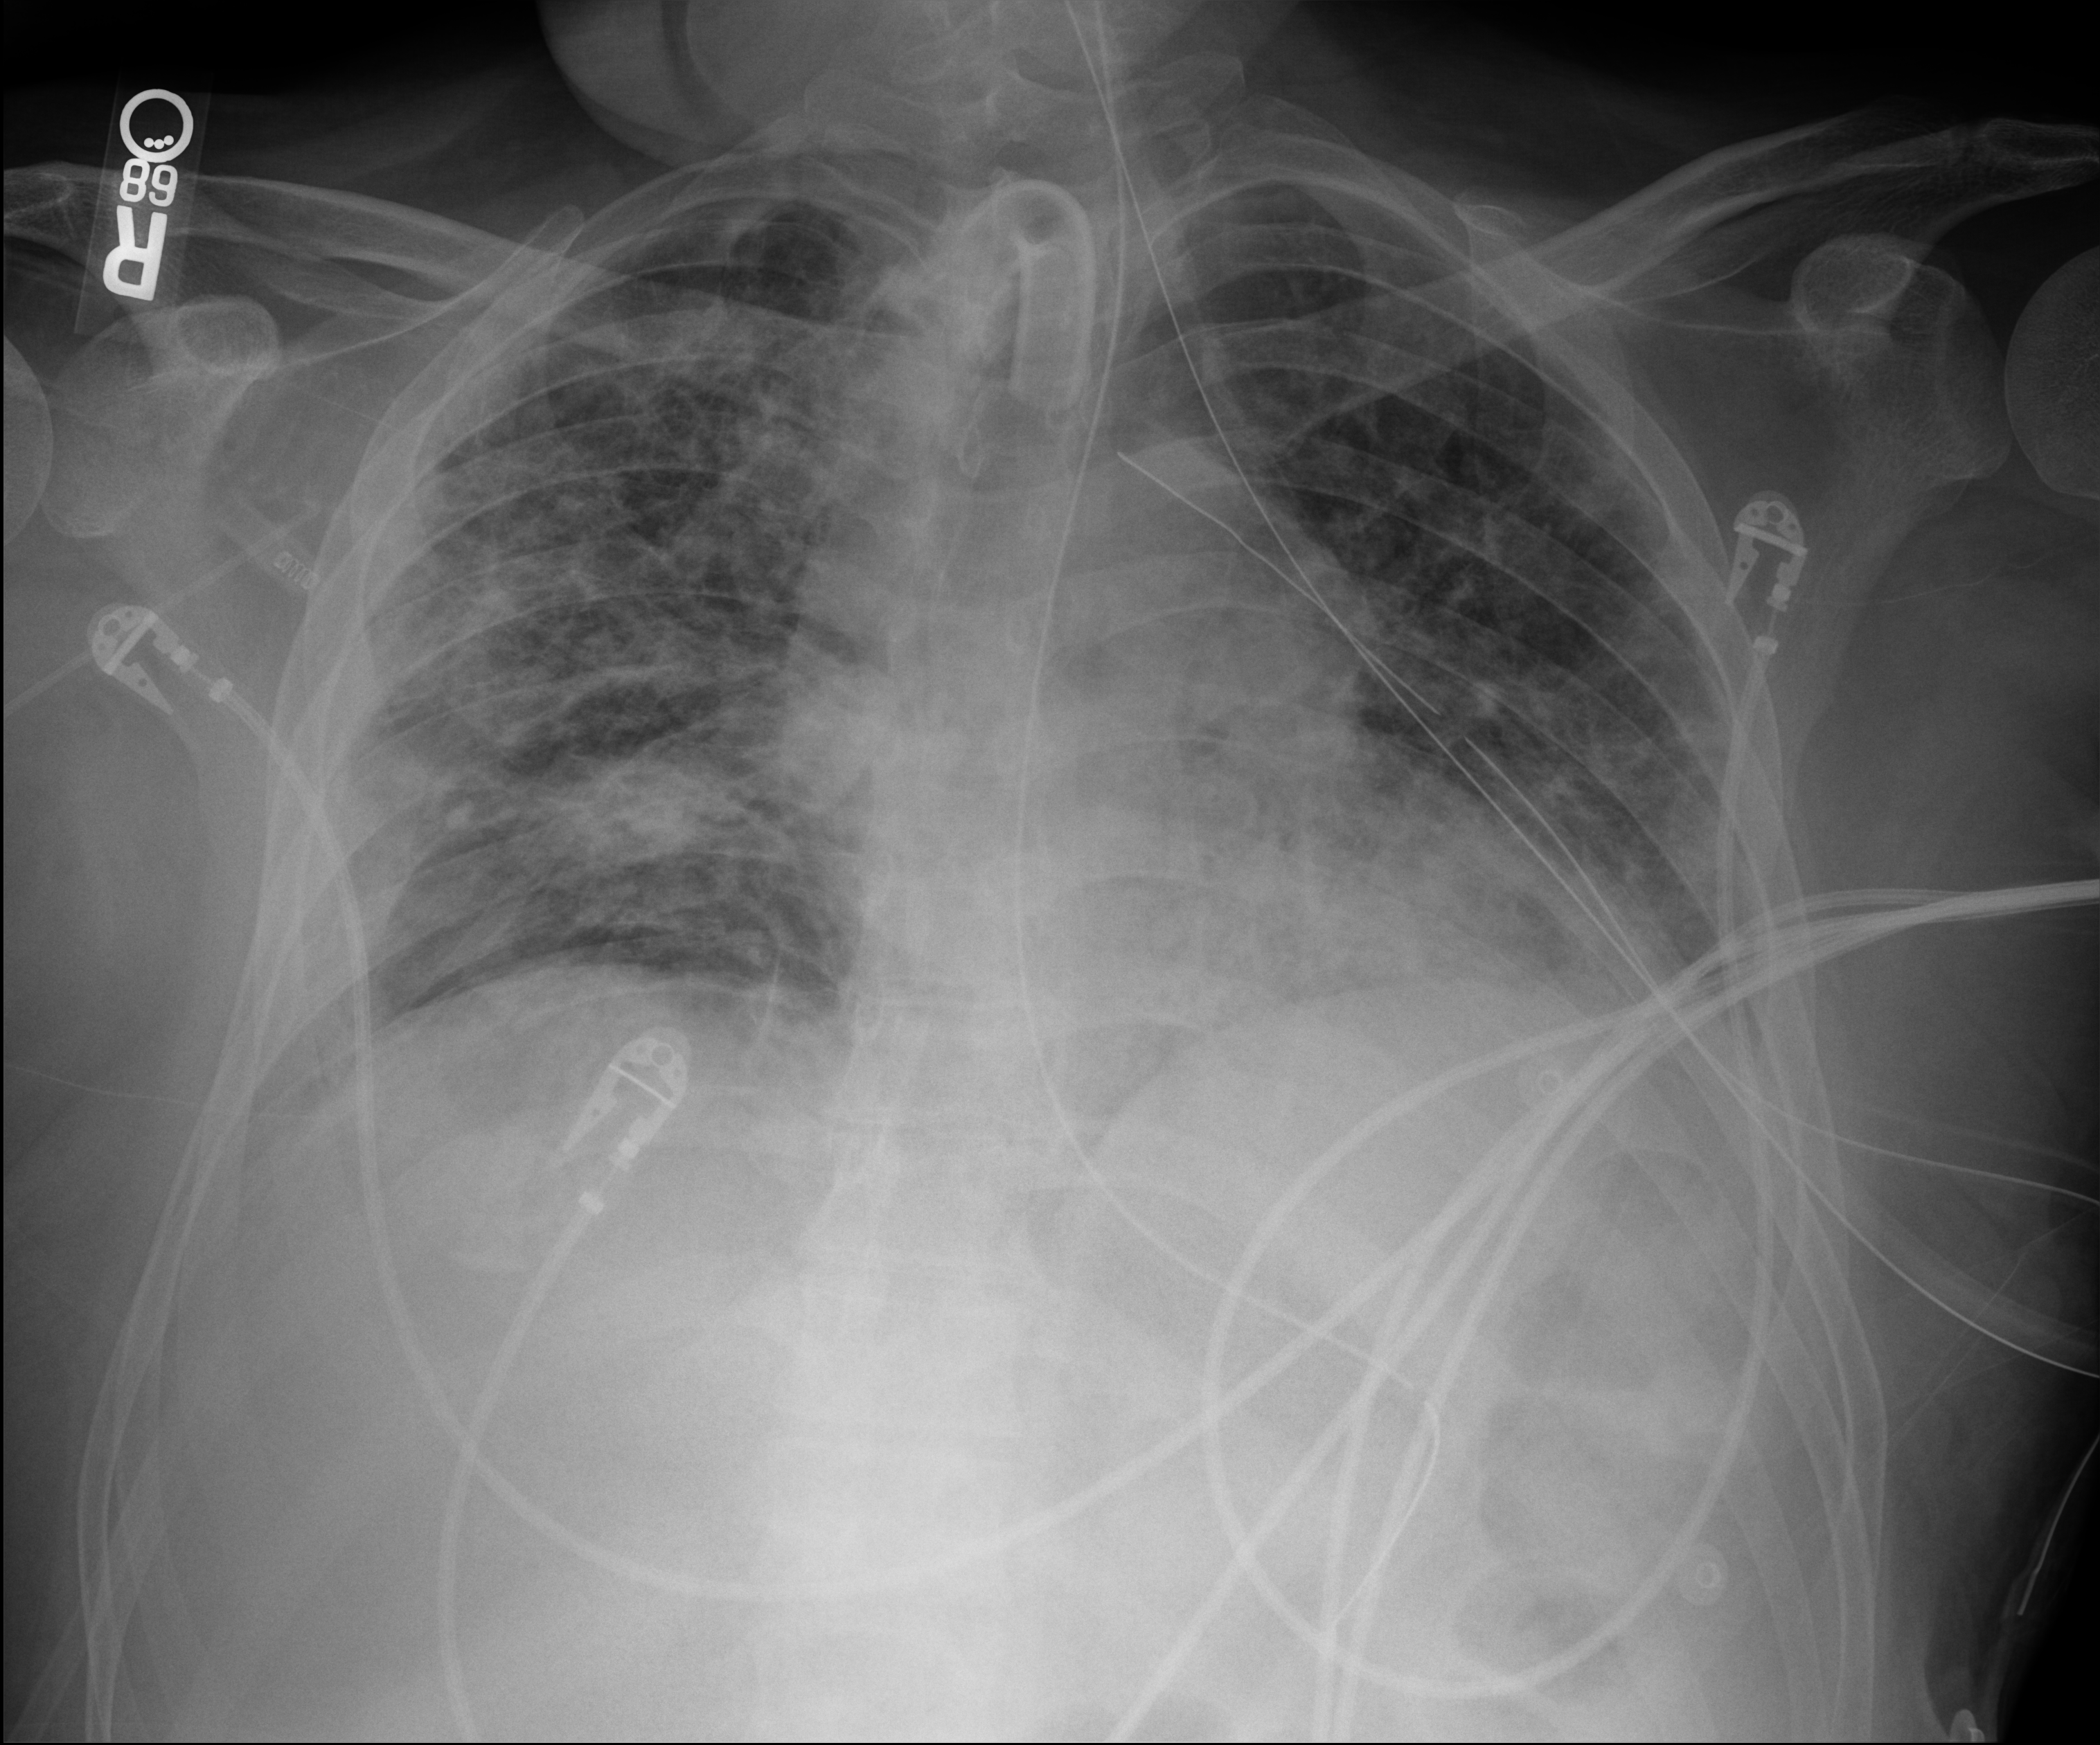
Chest radiograph. Patient hospitalised with COVID-19; male, aged 18–59 years.
From the hospital-stay record, not from the radiograph (when in the stay this image was taken is not recorded):
- diabetes (admission record): yes